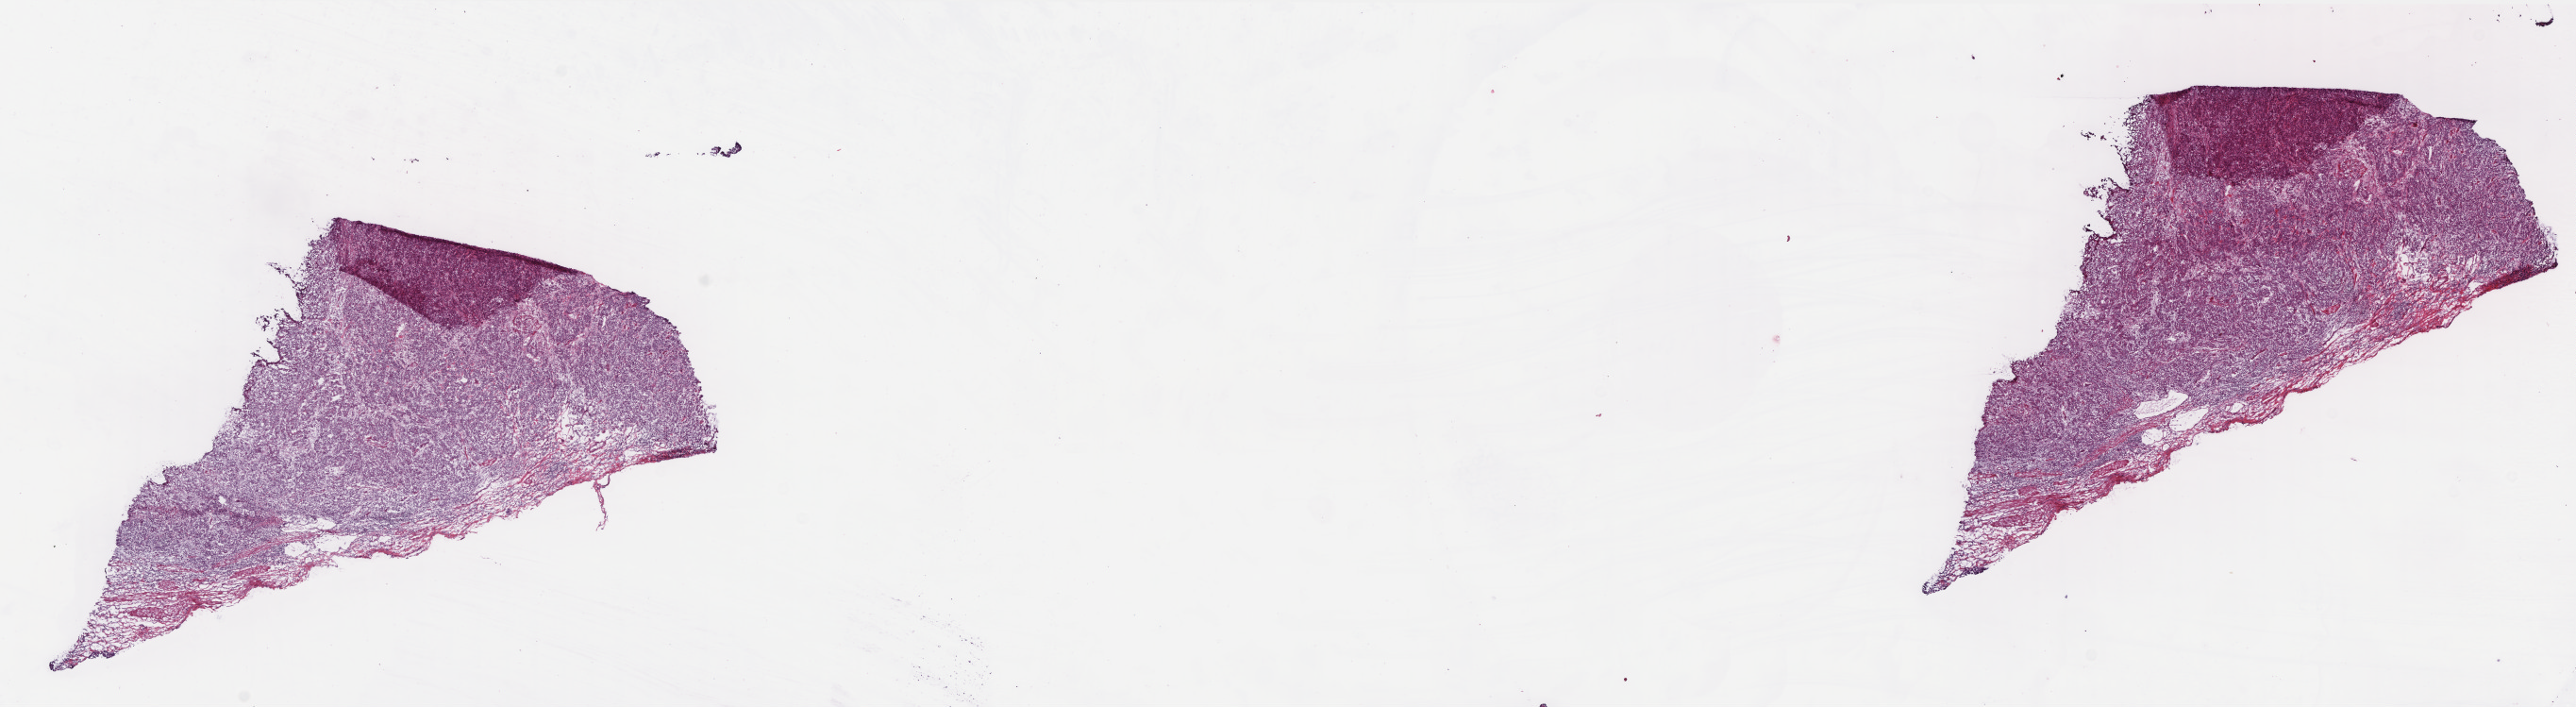
Digitized H&E-stained tissue section (whole slide), shown as a low-resolution overview of the whole scanned area (about 21.9 x 6.0 mm), frozen section, primary tumour sample from the colon. Female patient; age at initial diagnosis 84 years. Slide review estimates, as recorded: tumour cells 90%, tumour nuclei 80%, normal cells 0%, stromal cells 9%, necrosis 1%. Inflammatory infiltration, as recorded: lymphocyte infiltration 10%, monocyte infiltration 0%, neutrophil infiltration 5%.
- diagnosis: Adenocarcinoma, NOS (cecum)
- AJCC pathologic stage: IIA (6th edition)
- TNM: T3 N0 M0
- lymph nodes positive (case pathology): 0 of 18 examined